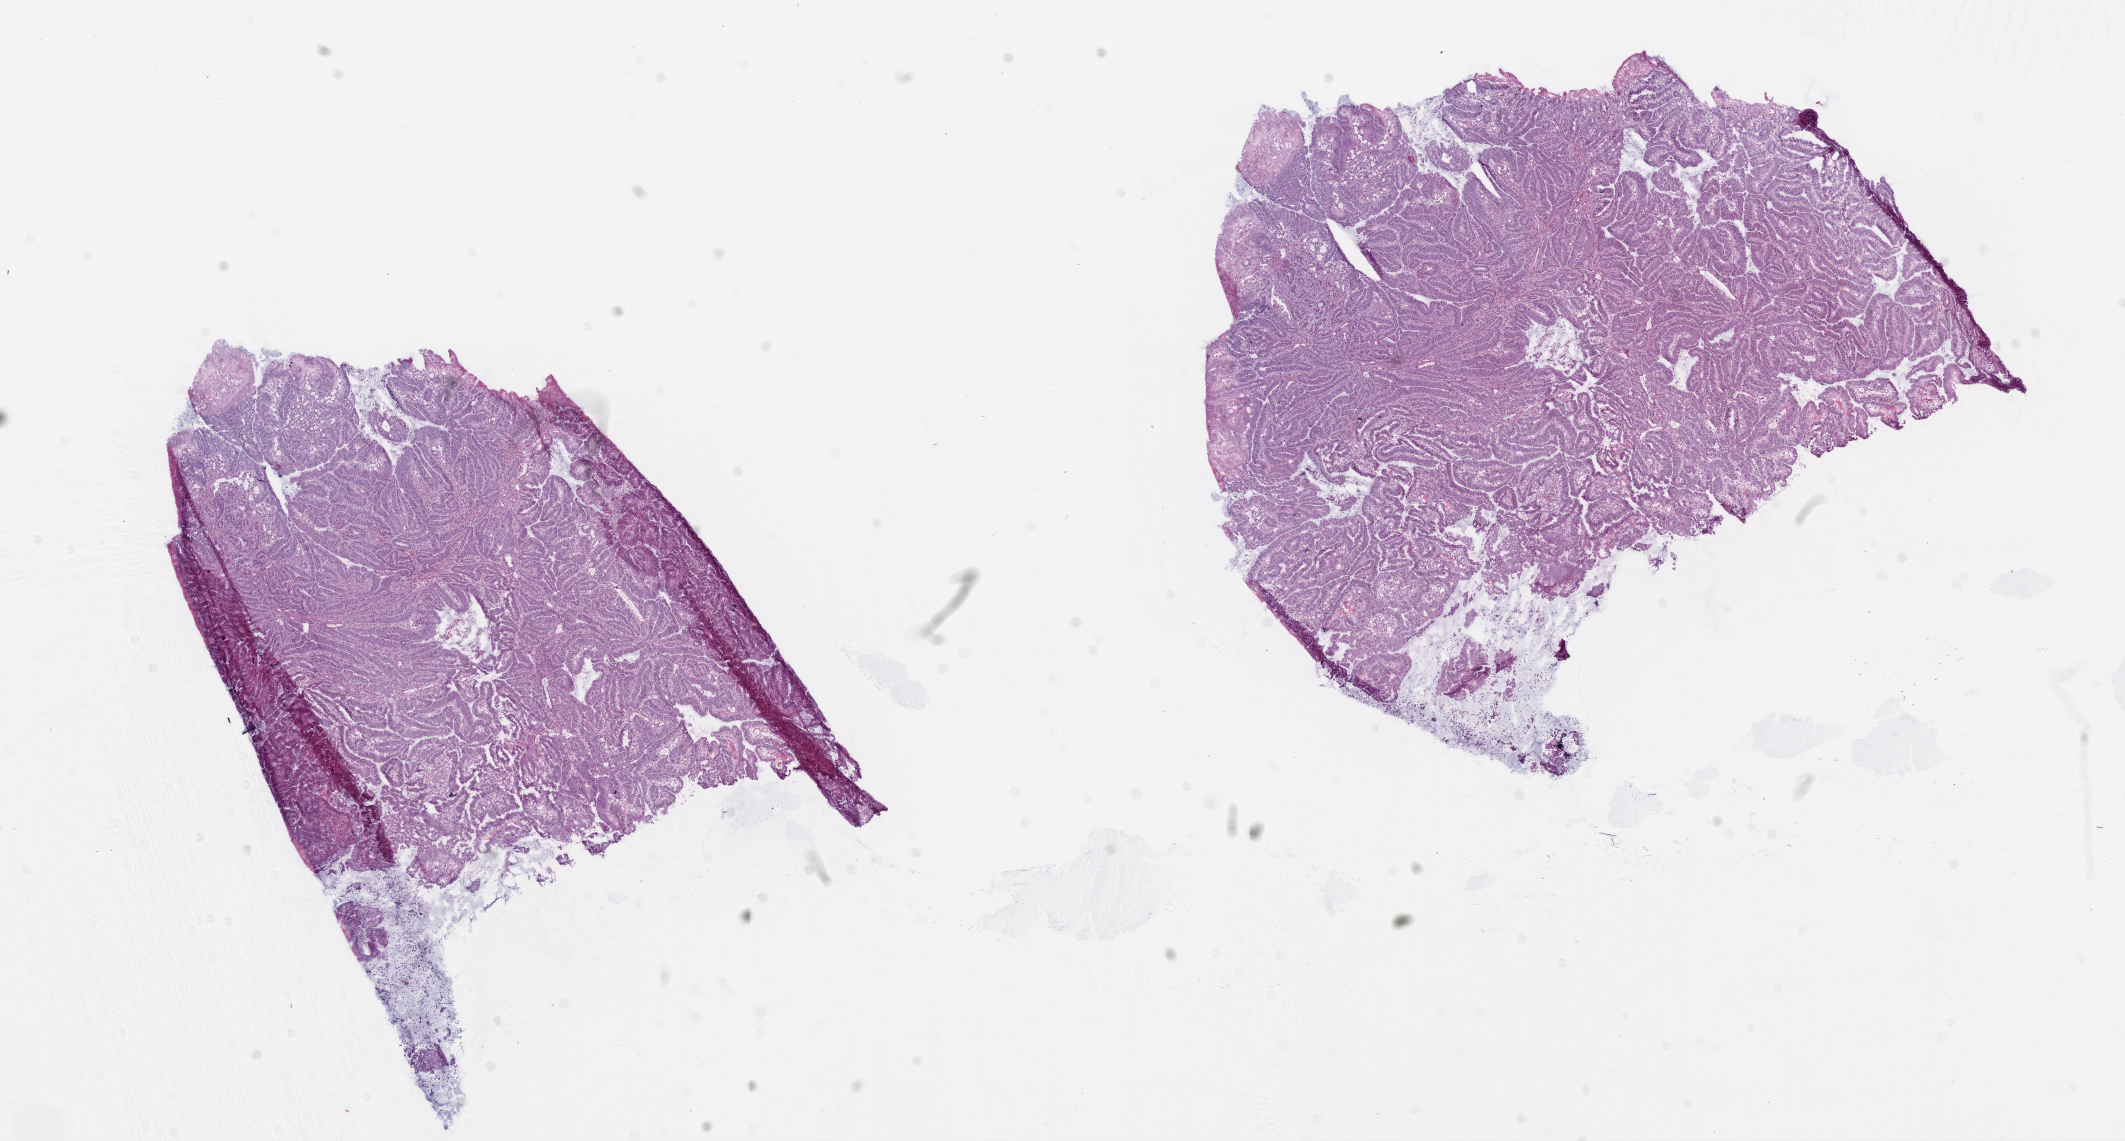
Digitized Hematoxylin and eosin (H&E) stained tissue section (whole slide) — whole scanned area (about 17.1 x 9.2 mm) shown as a low-resolution overview, frozen section, sample: primary tumour, colon. Female patient; age at initial diagnosis 81 years. Pathologist review of this section (percent, as recorded): tumour cells 90%, tumour nuclei 85%, normal cells 0%, stromal cells 5%, necrosis 5%.
* lymph nodes positive (case pathology): 0 of 13 examined
* pathologic diagnosis: Mucinous adenocarcinoma (ascending colon)
* AJCC pathologic stage: I (6th edition)